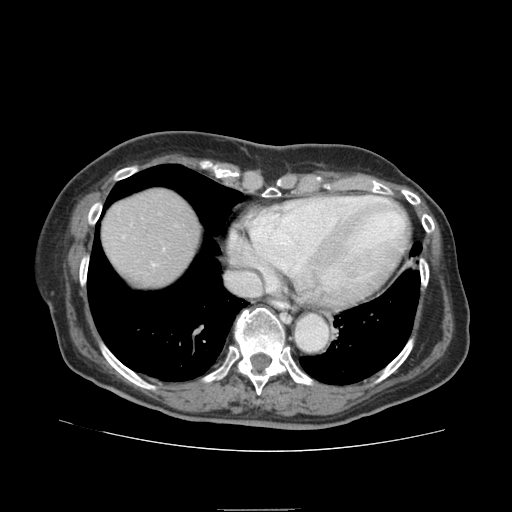
Contrast-enhanced abdominal CT (liver protocol), one axial slice. Slice 76 of 95 in the series (ordered by position). 140 kVp. Soft-tissue window (W 400 / L 40 HU). 512 × 512 image matrix, field of view 360 × 360 mm. Case-level facts recorded for this patient, not image findings: diagnosis: hepatocellular carcinoma (patient treated with transarterial chemoembolisation; whether this scan precedes or follows treatment is not stated here); TNM stage (as recorded): Stage-IVA.
Structures marked on this image (semi-automatic segmentation, software-assisted and operator-edited):
- abdominal aorta: box from (x=296, y=314) to (x=327, y=351) px
- liver parenchyma outside the tumour (the mass and vessels are separate outlines, so this box may not span the whole liver): (x=102, y=190)–(x=200, y=286)
- liver vessels: (x=153, y=264)–(x=155, y=266)